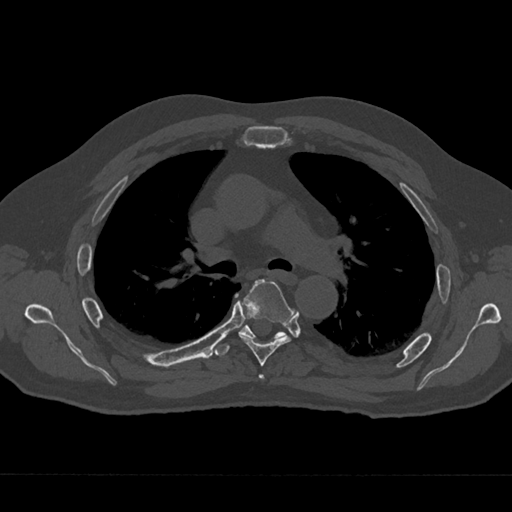
CT including the spine, one axial slice; position 457 of 797 along the scan axis; reconstruction kernel Br40s/3; 120 kVp; bone window (W 1800 / L 400 HU); 0.5 mm slice thickness; 512 × 512 image matrix, field of view 377 × 377 mm. Patient: male, 75 years. Case-level facts recorded for this patient, not image findings: primary cancer: renal; vertebrae with lytic lesions (as recorded): T4.
Outlined on this slice (semi-automatically segmented with operator editing):
- T4 vertebra: bounding box [x1, y1, x2, y2] px = [258, 374, 264, 380]
- T5 vertebra: [239, 279, 293, 366]
- T6 vertebra: [216, 319, 286, 357]